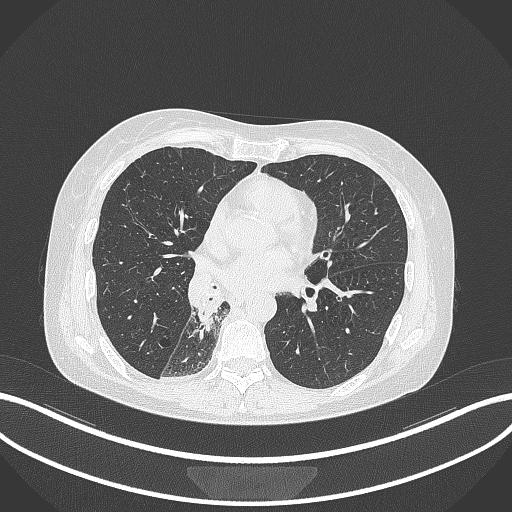
Chest CT, one axial slice. Position 143 of 329 along the scan axis. Lung window (W 1500 / L -600 HU). 1 mm slice thickness. 512 × 512 image matrix, field of view 400 × 400 mm. Female patient, age 63 years. Case-level facts recorded for this patient, not image findings: clinical TNM (as recorded): T1c N0 M0.
Outlined on this slice (rectangle marked by the reading radiologist):
- lung tumour (recorded histology: adenocarcinoma): bounding box (x1, y1, x2, y2) in pixels: (194, 282, 225, 339)